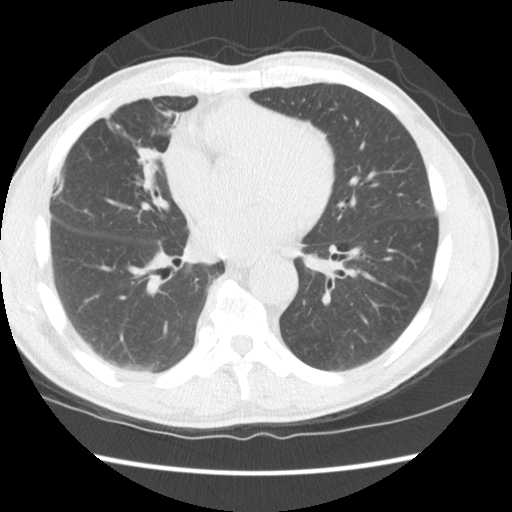
Chest CT (low-dose screening protocol), one axial image, third annual screen, lung window (W 1500 / L -600 HU), standard (soft-tissue) reconstruction kernel (STANDARD), 120 kVp, slice 64 of 147 in the series. Male, age 65 years at enrolment.
Expert-annotated lung lesion, bounding box [x1, y1, x2, y2] px = [107, 132, 172, 208]. Screening reader's record for this exam (one nodule recorded; not confirmed to be the boxed lesion): non-calcified nodule or mass ≥4 mm, right middle lobe, 16 × 15 mm, smooth margins, soft tissue attenuation, pre-existing on the prior screen: yes; interval growth: yes. Official screen result: positive, other.